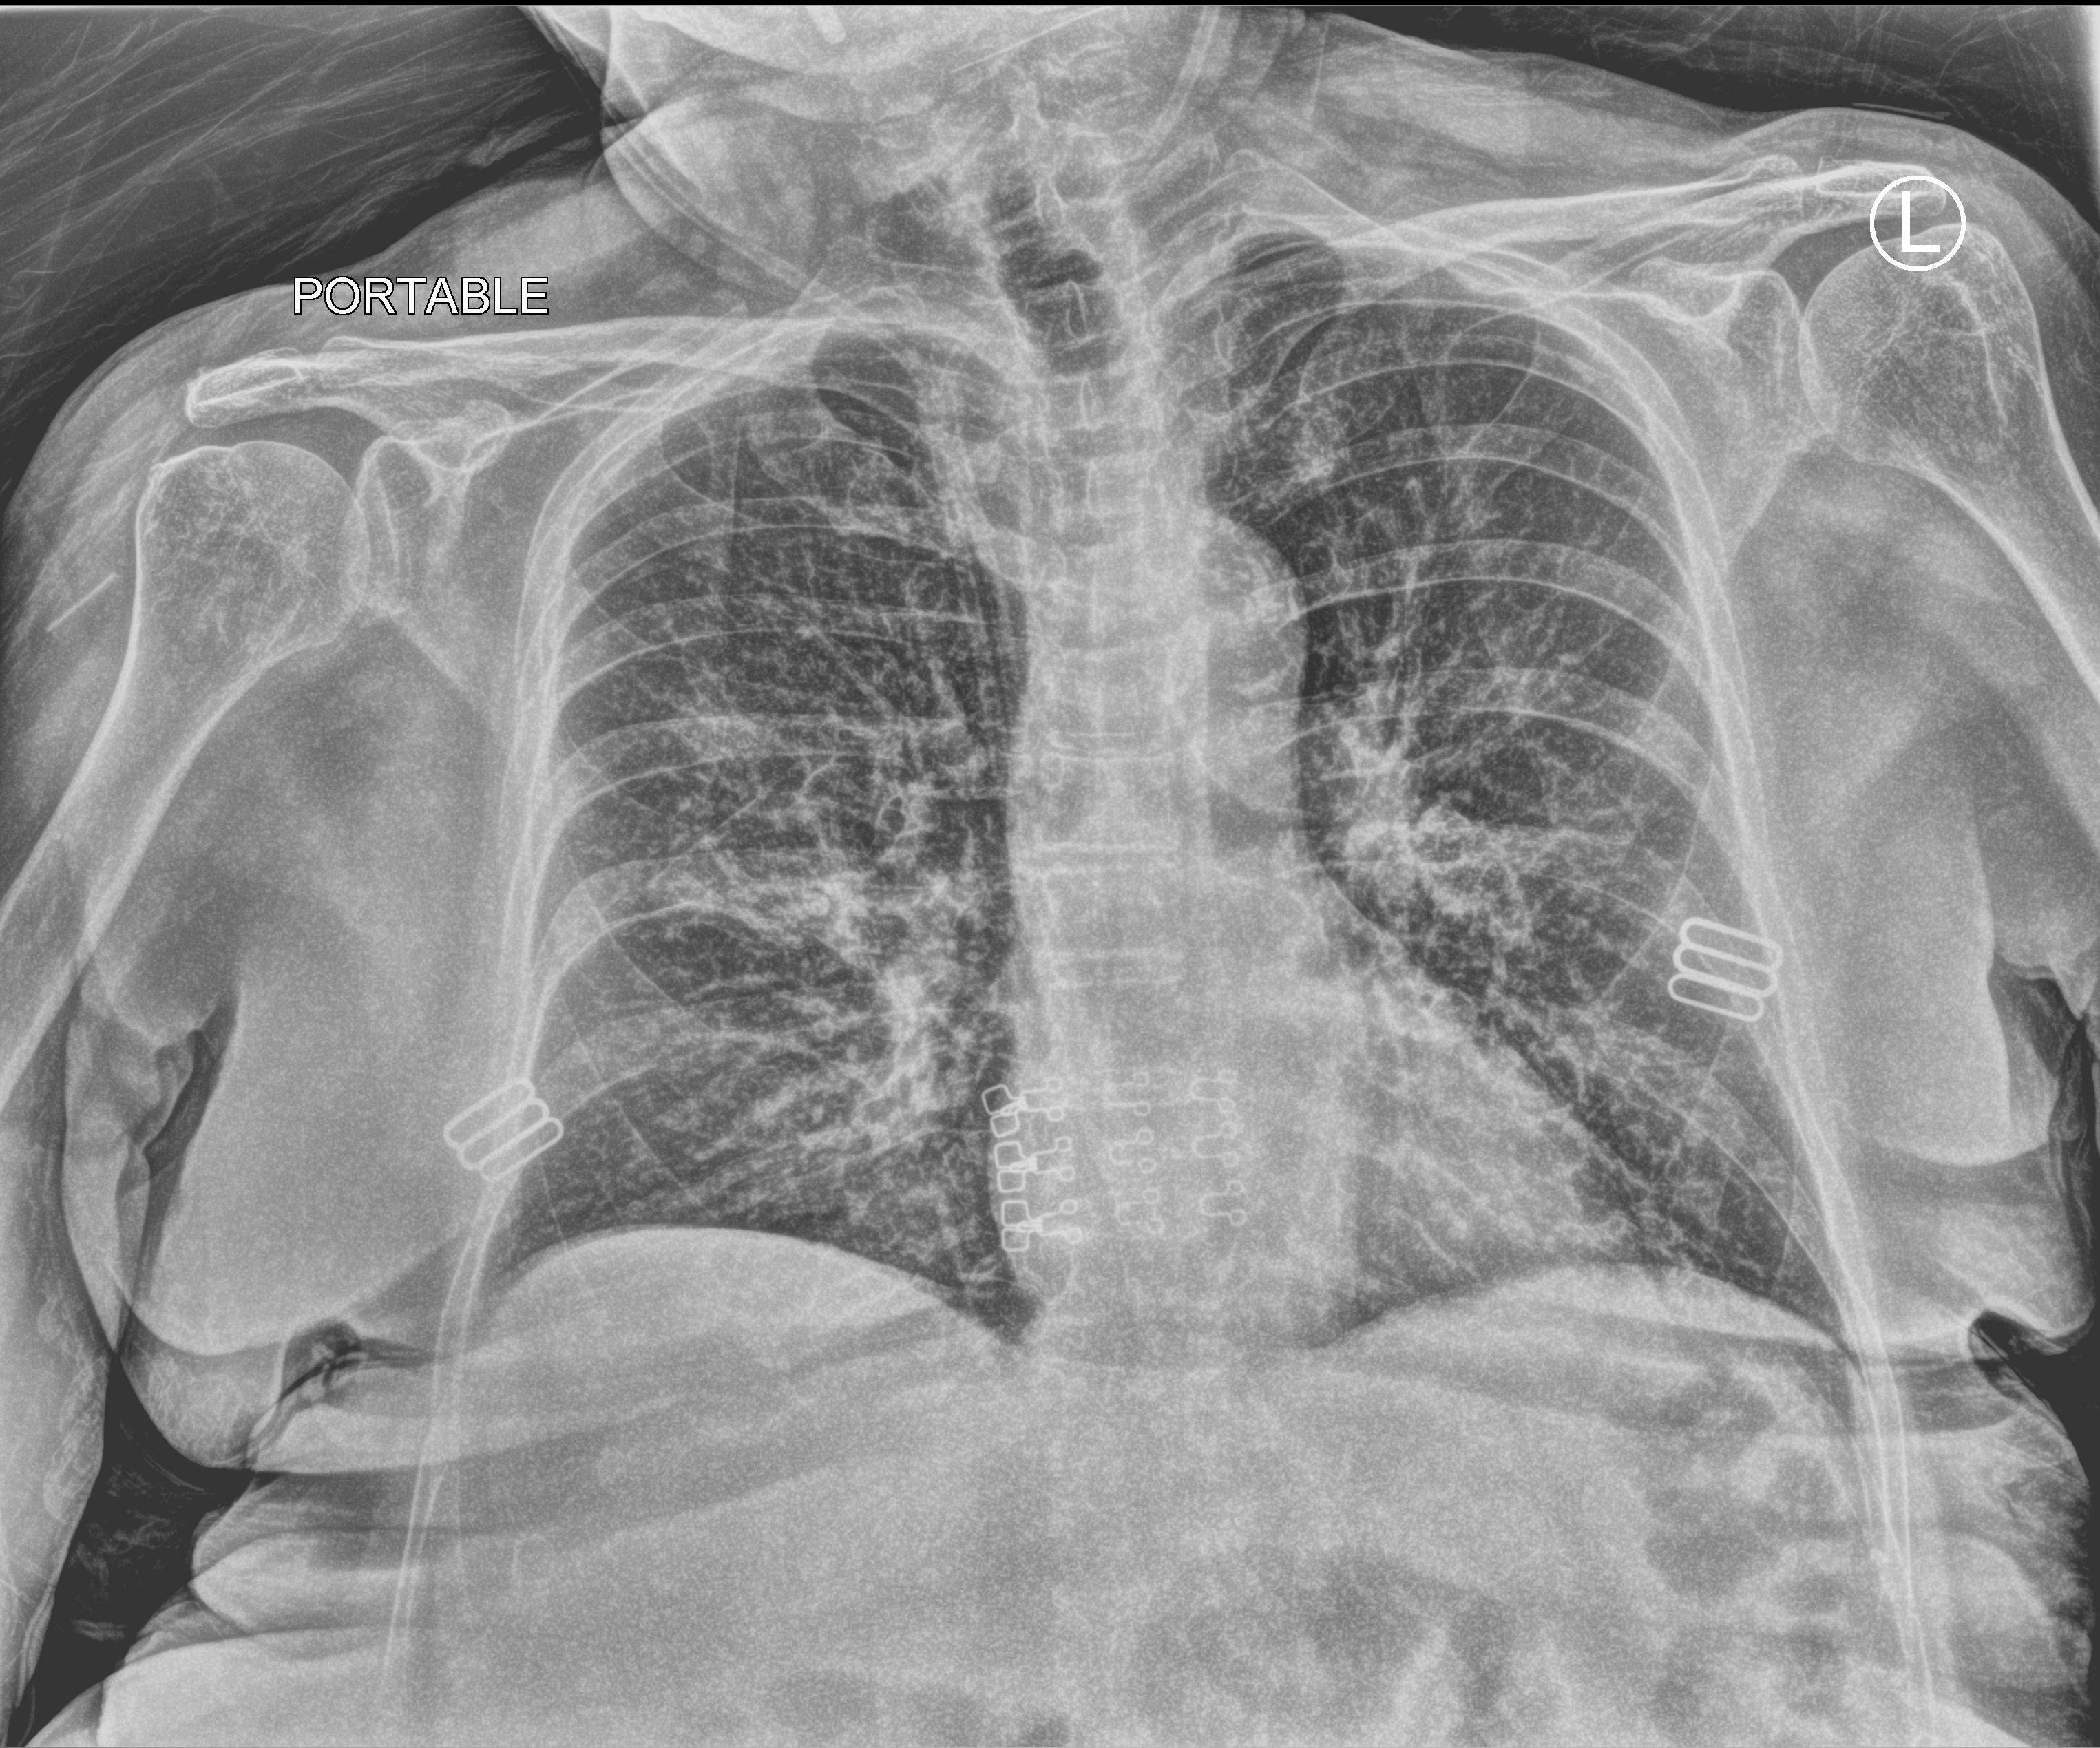
Chest X-ray (portable); anteroposterior (AP) projection. Female patient hospitalised with COVID-19, age 75–90 years.
Admission-level facts for this patient (not findings on this image; timing relative to this image not recorded):
- smoking status (admission record): former
- mechanically ventilated during this hospital stay: no
- diabetes (admission record): no